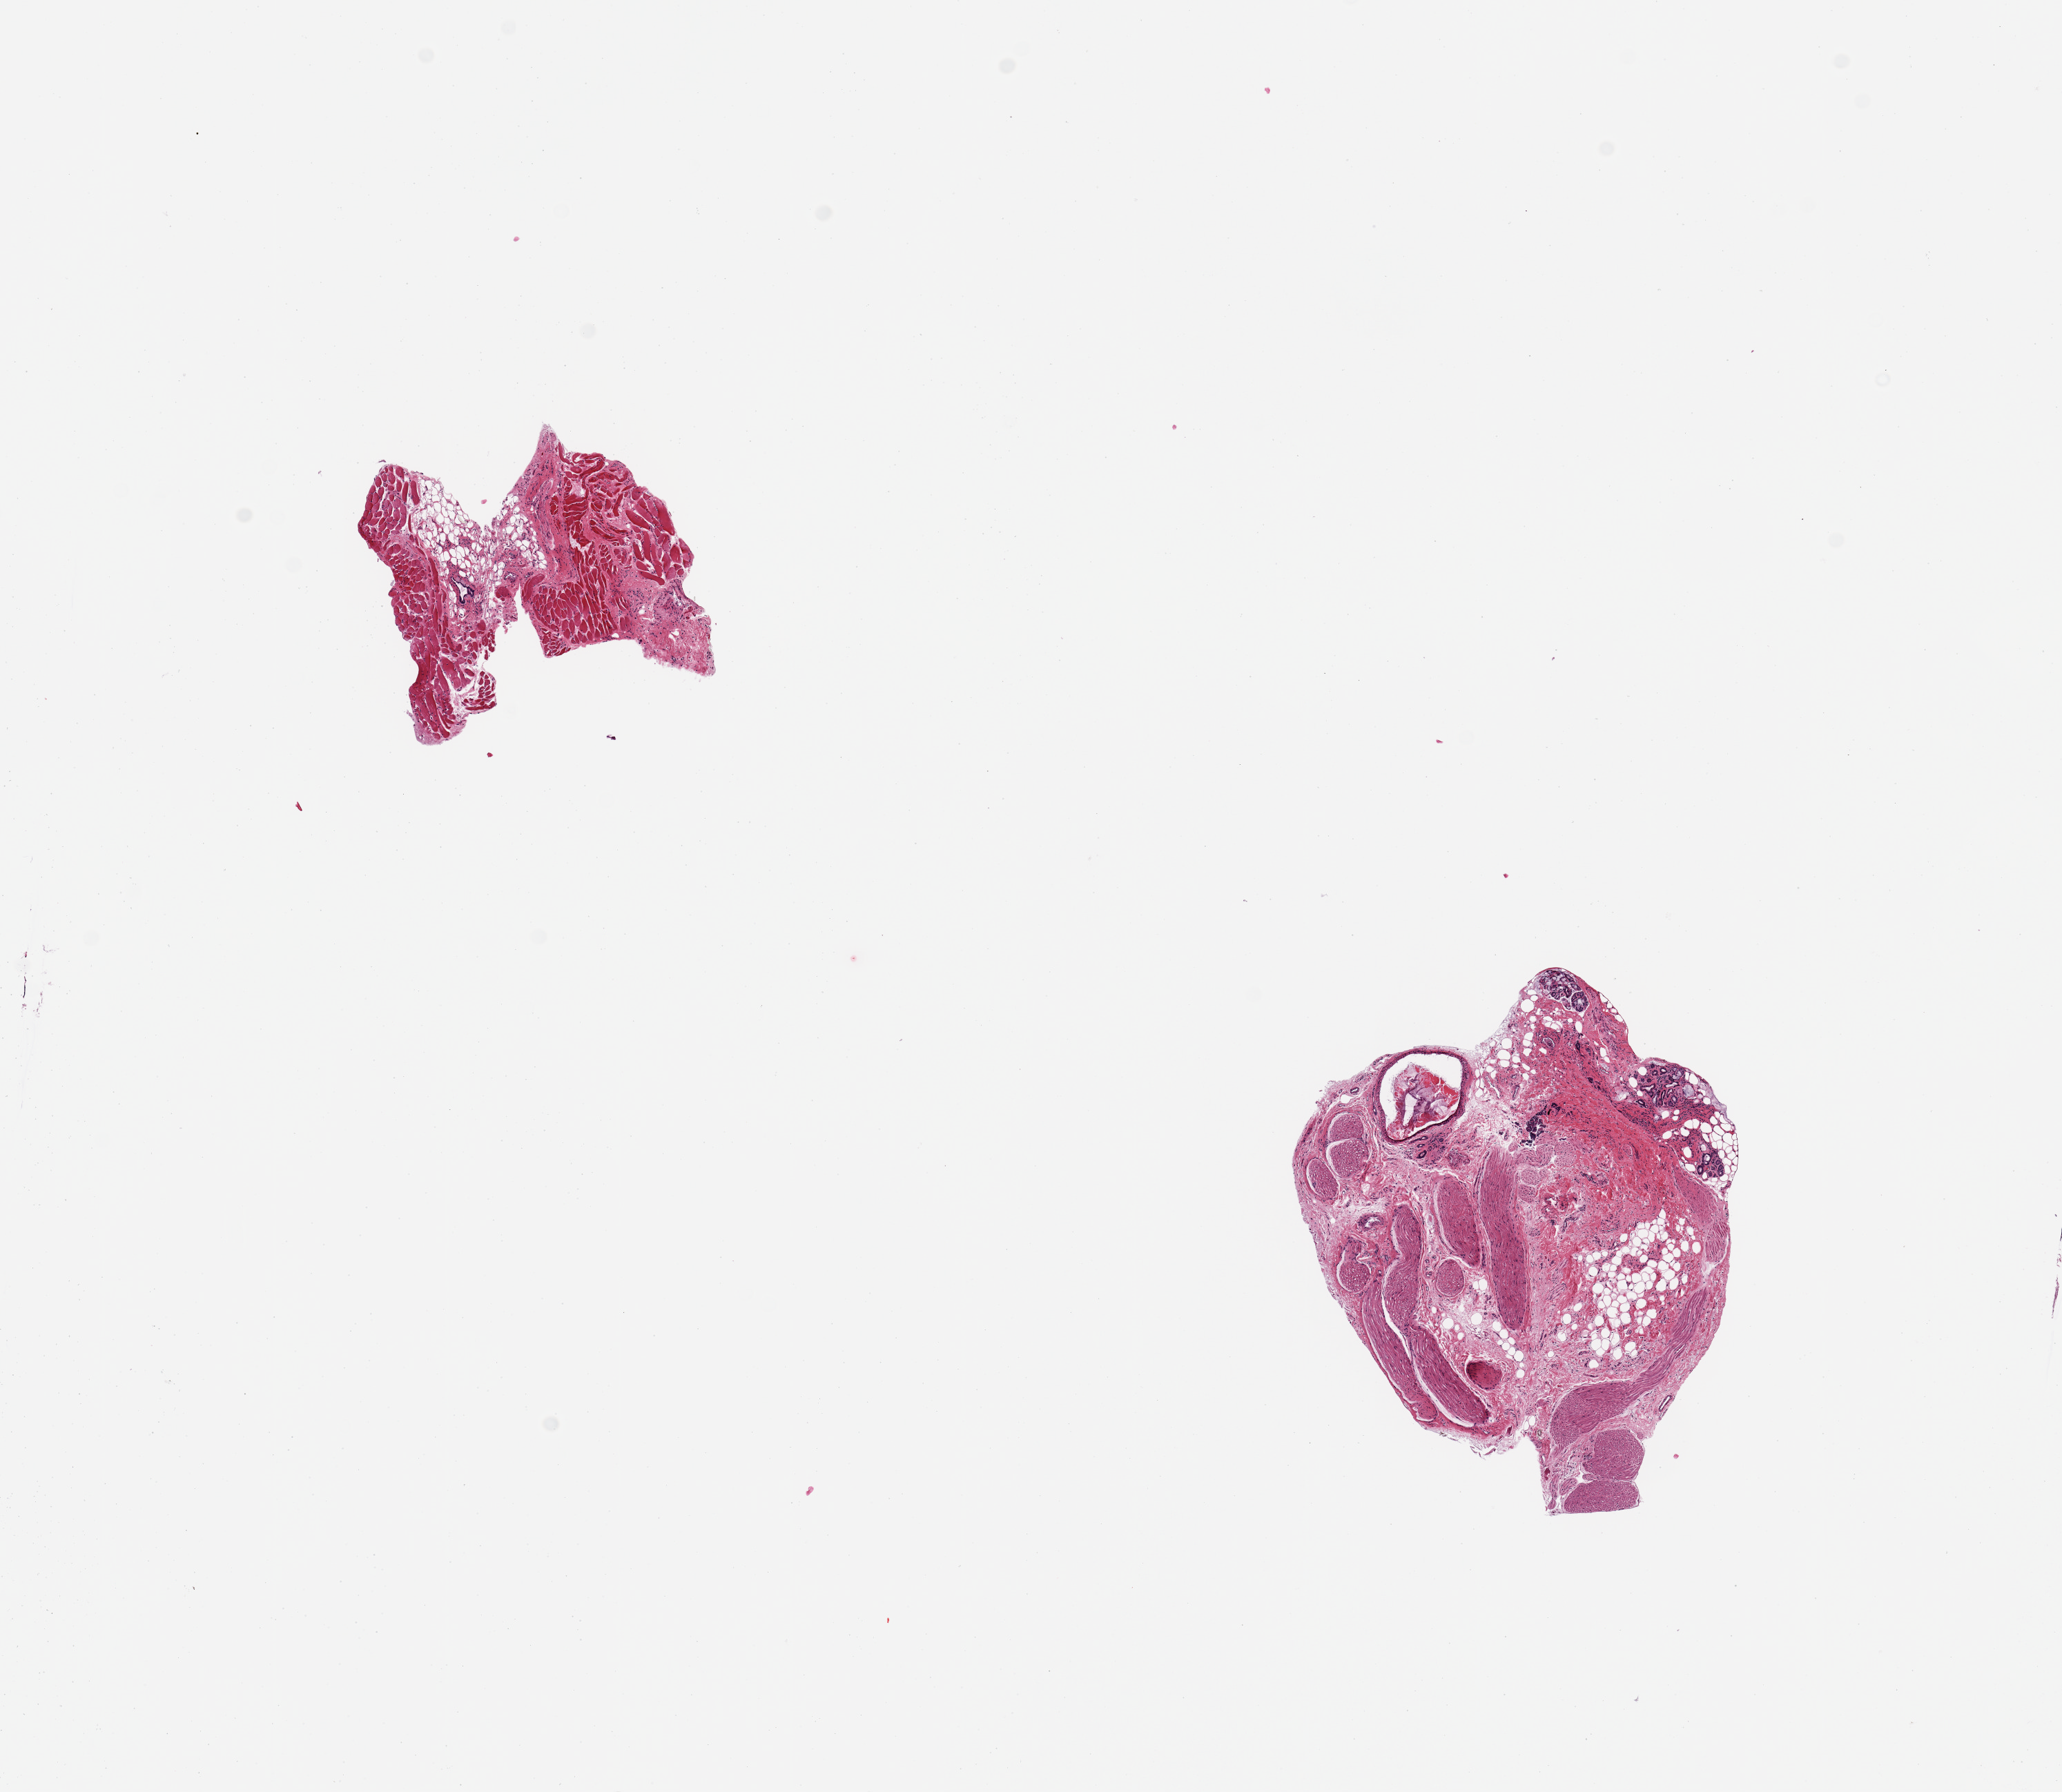
Whole-slide image, H&E stain, brightfield, a low-resolution overview of the entire scanned area, about 11.8 x 10.3 mm (slide scanned at 20x); PAXgene-fixed paraffin-embedded (PFPE) section; section of minor salivary gland (target tissue); tissue donor sample. Donor sex: male.
* review note (as recorded): 2 pieces; larger contains nerves and fat with 5% salivary gland tissue; smaller is skeletal muscle and fat with 1 duct